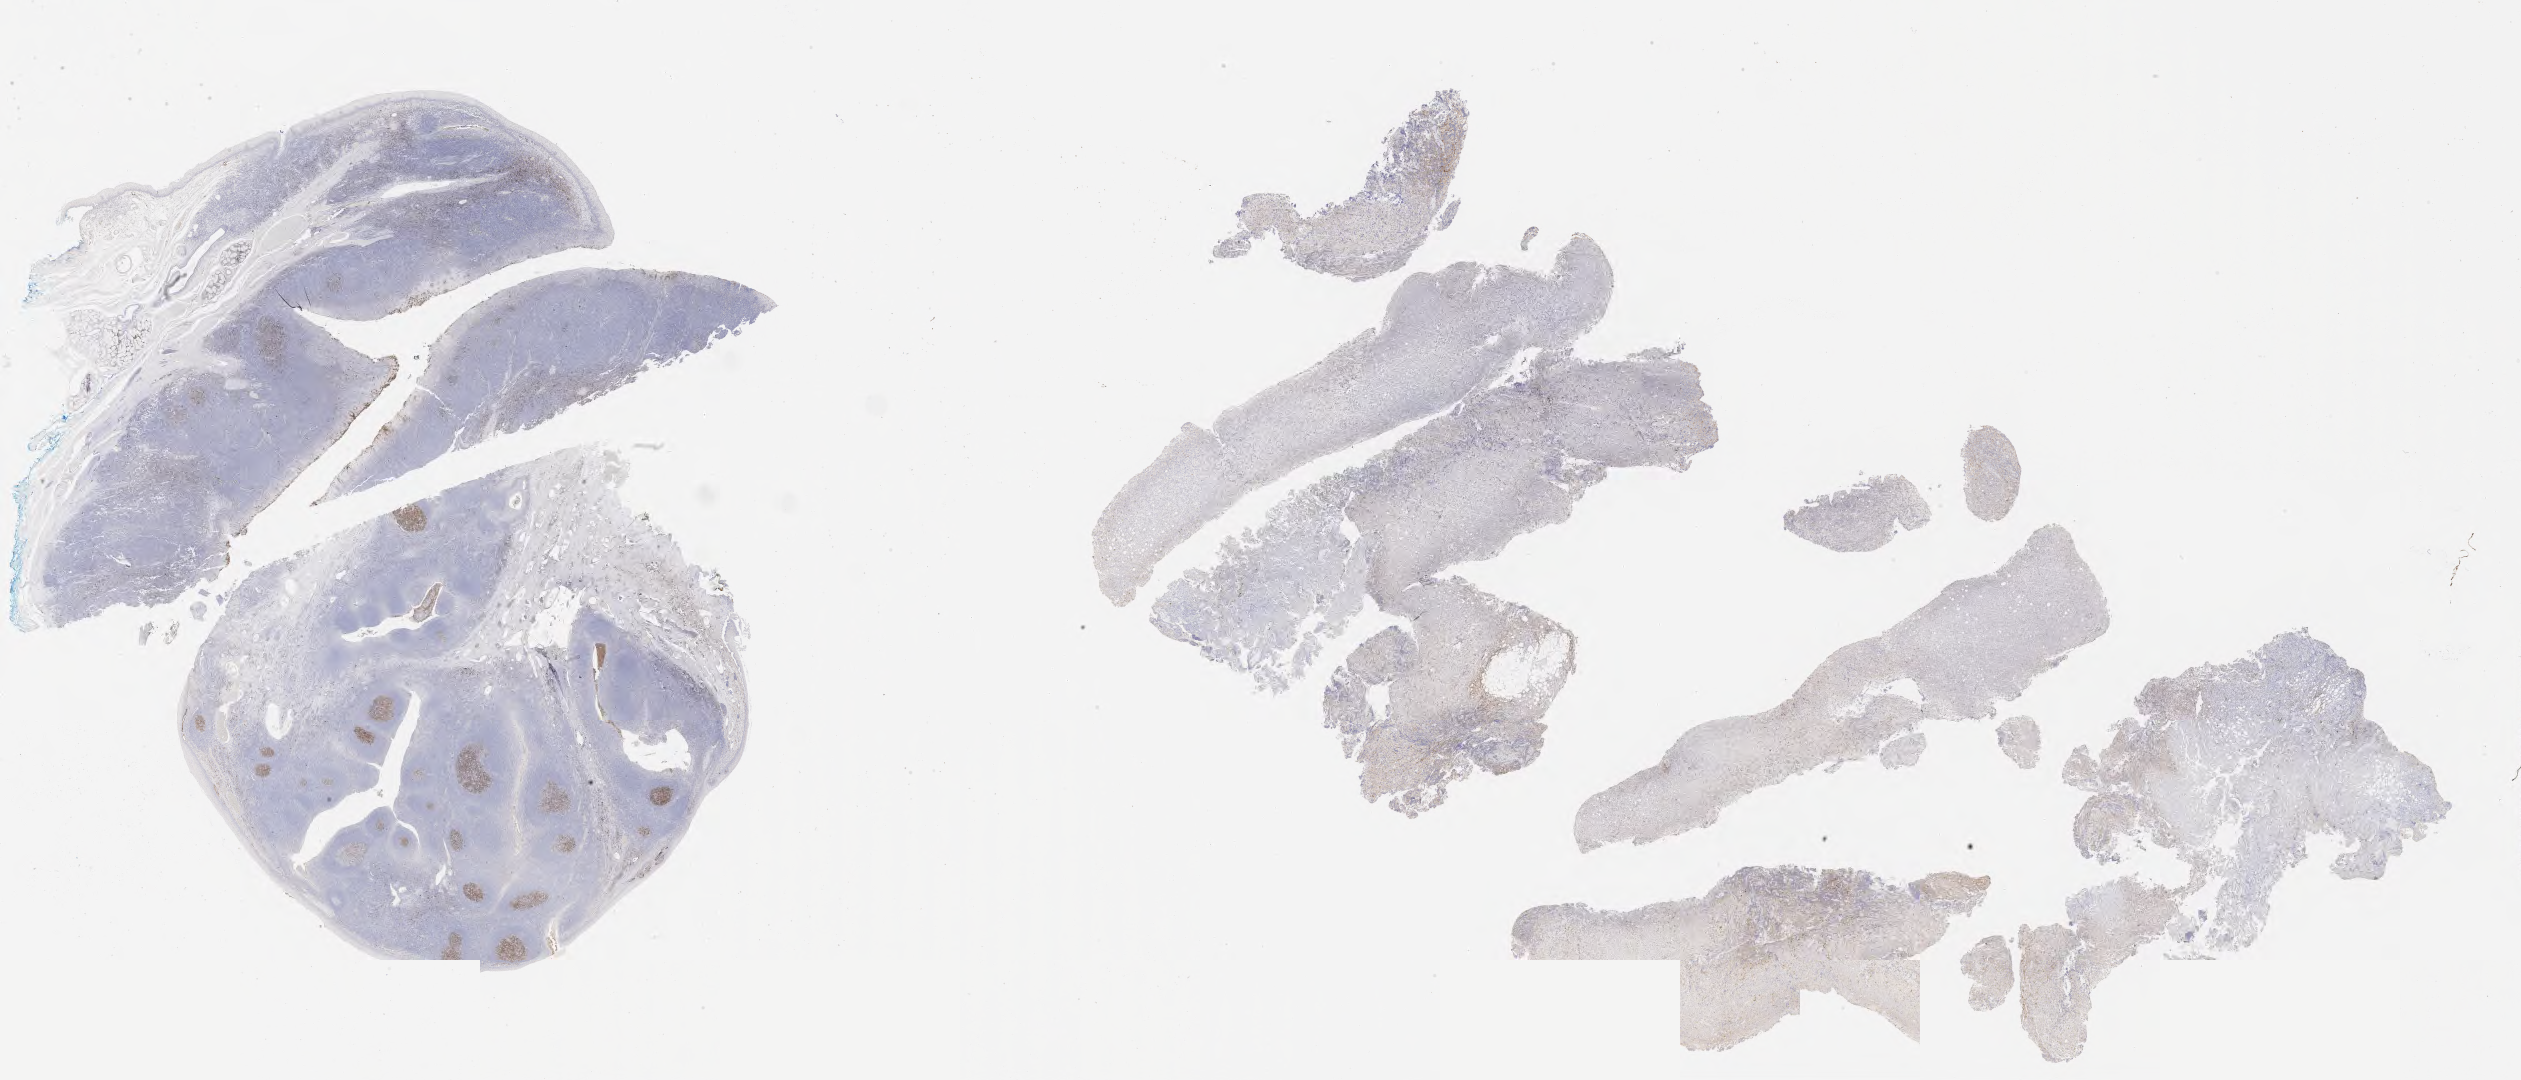
Whole-slide image, immunohistochemical stain for CD10, a low-resolution overview of the entire scanned area, about 40.8 x 17.5 mm. Specimen: tumor tissue. Patient: male, aged 45.
Diagnosis: Diffuse large B-cell lymphoma, NOS.